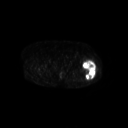
FDG PET of an extremity soft-tissue mass (from a PET/CT study), one axial slice. Position 247 of 267 along the scan axis. 3.27 mm slice thickness. 128 × 128 image matrix, field of view 700 × 700 mm. Patient: female, 62 years. From the clinical record (not read from this slice): histological type: undifferentiated – high grade; grade: high; site of the primary tumour: left thigh.
Annotated regions visible in this slice (expert contour drawn on MRI and transferred to this co-registered scan by the dataset authors):
- gross tumour volume including surrounding oedema: bounding box <82,60,96,80> (left, top, right, bottom; pixels)
- gross tumour volume (mass): <82,61,96,80>